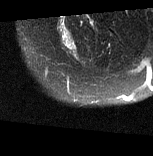
MRI of an extremity soft-tissue mass, one axial slice. T2-weighted fat-saturated. MR volume resampled by the dataset authors to the PET/CT grid (not the native acquisition matrix). 3.27 mm slice thickness. 153 × 156 image matrix, field of view 149 × 152 mm. Female patient. From the clinical record (not read from this slice): histological type: synovial sarcoma; grade: intermediate; site of the primary tumour: right buttock.
Structures marked on this image (expert contour drawn on MRI and transferred to this co-registered scan by the dataset authors):
- gross tumour volume including surrounding oedema: bounding box <58,20,77,55> (left, top, right, bottom; pixels)